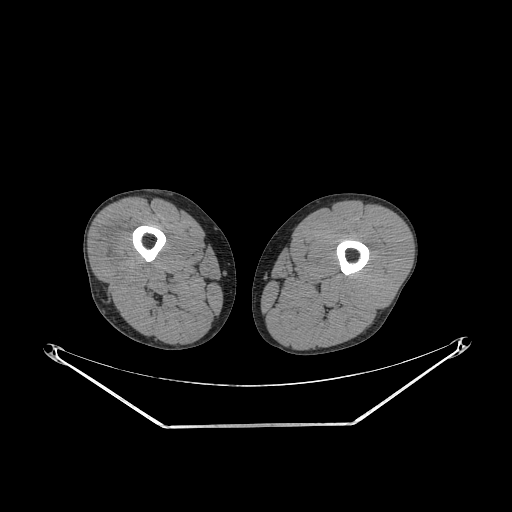
CT of an extremity soft-tissue mass (from a PET/CT study), one axial slice. Slice 219 of 267 in the series (ordered by position). Soft-tissue window (W 400 / L 40 HU). 3.75 mm slice thickness. 512 × 512 image matrix, field of view 500 × 500 mm. Male patient. From the clinical record (not read from this slice): histological type: poorly differentiated synovial sarcoma; grade: high; site of the primary tumour: right buttock.
Annotated regions visible in this slice (expert contour drawn on MRI and transferred to this co-registered scan by the dataset authors):
- gross tumour volume including surrounding oedema: bounding box [x1, y1, x2, y2] px = [103, 235, 133, 268]